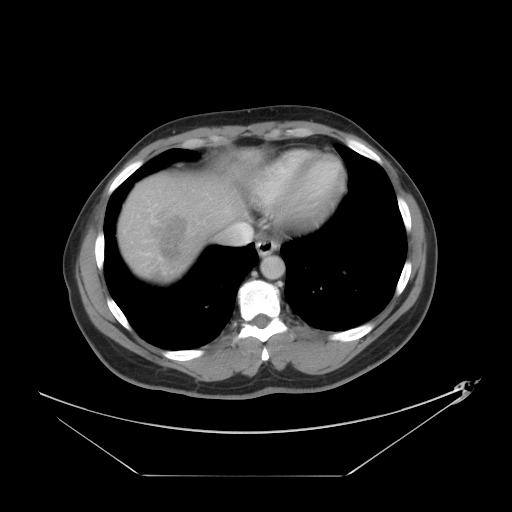
Contrast-enhanced abdominal CT, one axial slice. Slice 38 of 44 in the series (ordered by position). Reconstruction kernel STANDARD. Intravenous contrast given. Soft-tissue window (W 400 / L 40 HU). 5 mm slice thickness. 512 × 512 image matrix, field of view 466 × 466 mm. Male patient, age 49 years. From the clinical record (not read from this slice): diagnosis: colorectal cancer liver metastases, imaged before liver resection; multiple liver metastases: no; largest metastasis: 8.5 cm.
Structures marked on this image (expert manual segmentation):
- liver: box from (x=116, y=150) to (x=265, y=284) px
- planned liver remnant (the part of the liver to remain after resection): (x=205, y=150)–(x=264, y=228)
- liver metastasis: (x=153, y=216)–(x=185, y=282)